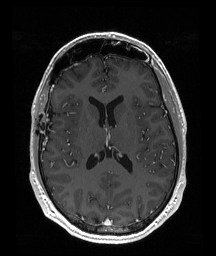
Brain MRI from a brain-tumour surgery series, one axial slice. Slice 93 of 192 in the series (ordered by position). T1-weighted post-contrast. 1 mm slice thickness. 216 × 256 image matrix, field of view 219 × 260 mm. Case-level facts recorded for this patient, not image findings: histopathology: Astrocytoma; WHO grade: 2; IDH mutation: yes; tumour location: Right Insular.
Annotated regions visible in this slice (outlined manually by an expert reader):
- tumour: bounding box (x1, y1, x2, y2) in pixels: (75, 114, 78, 118)